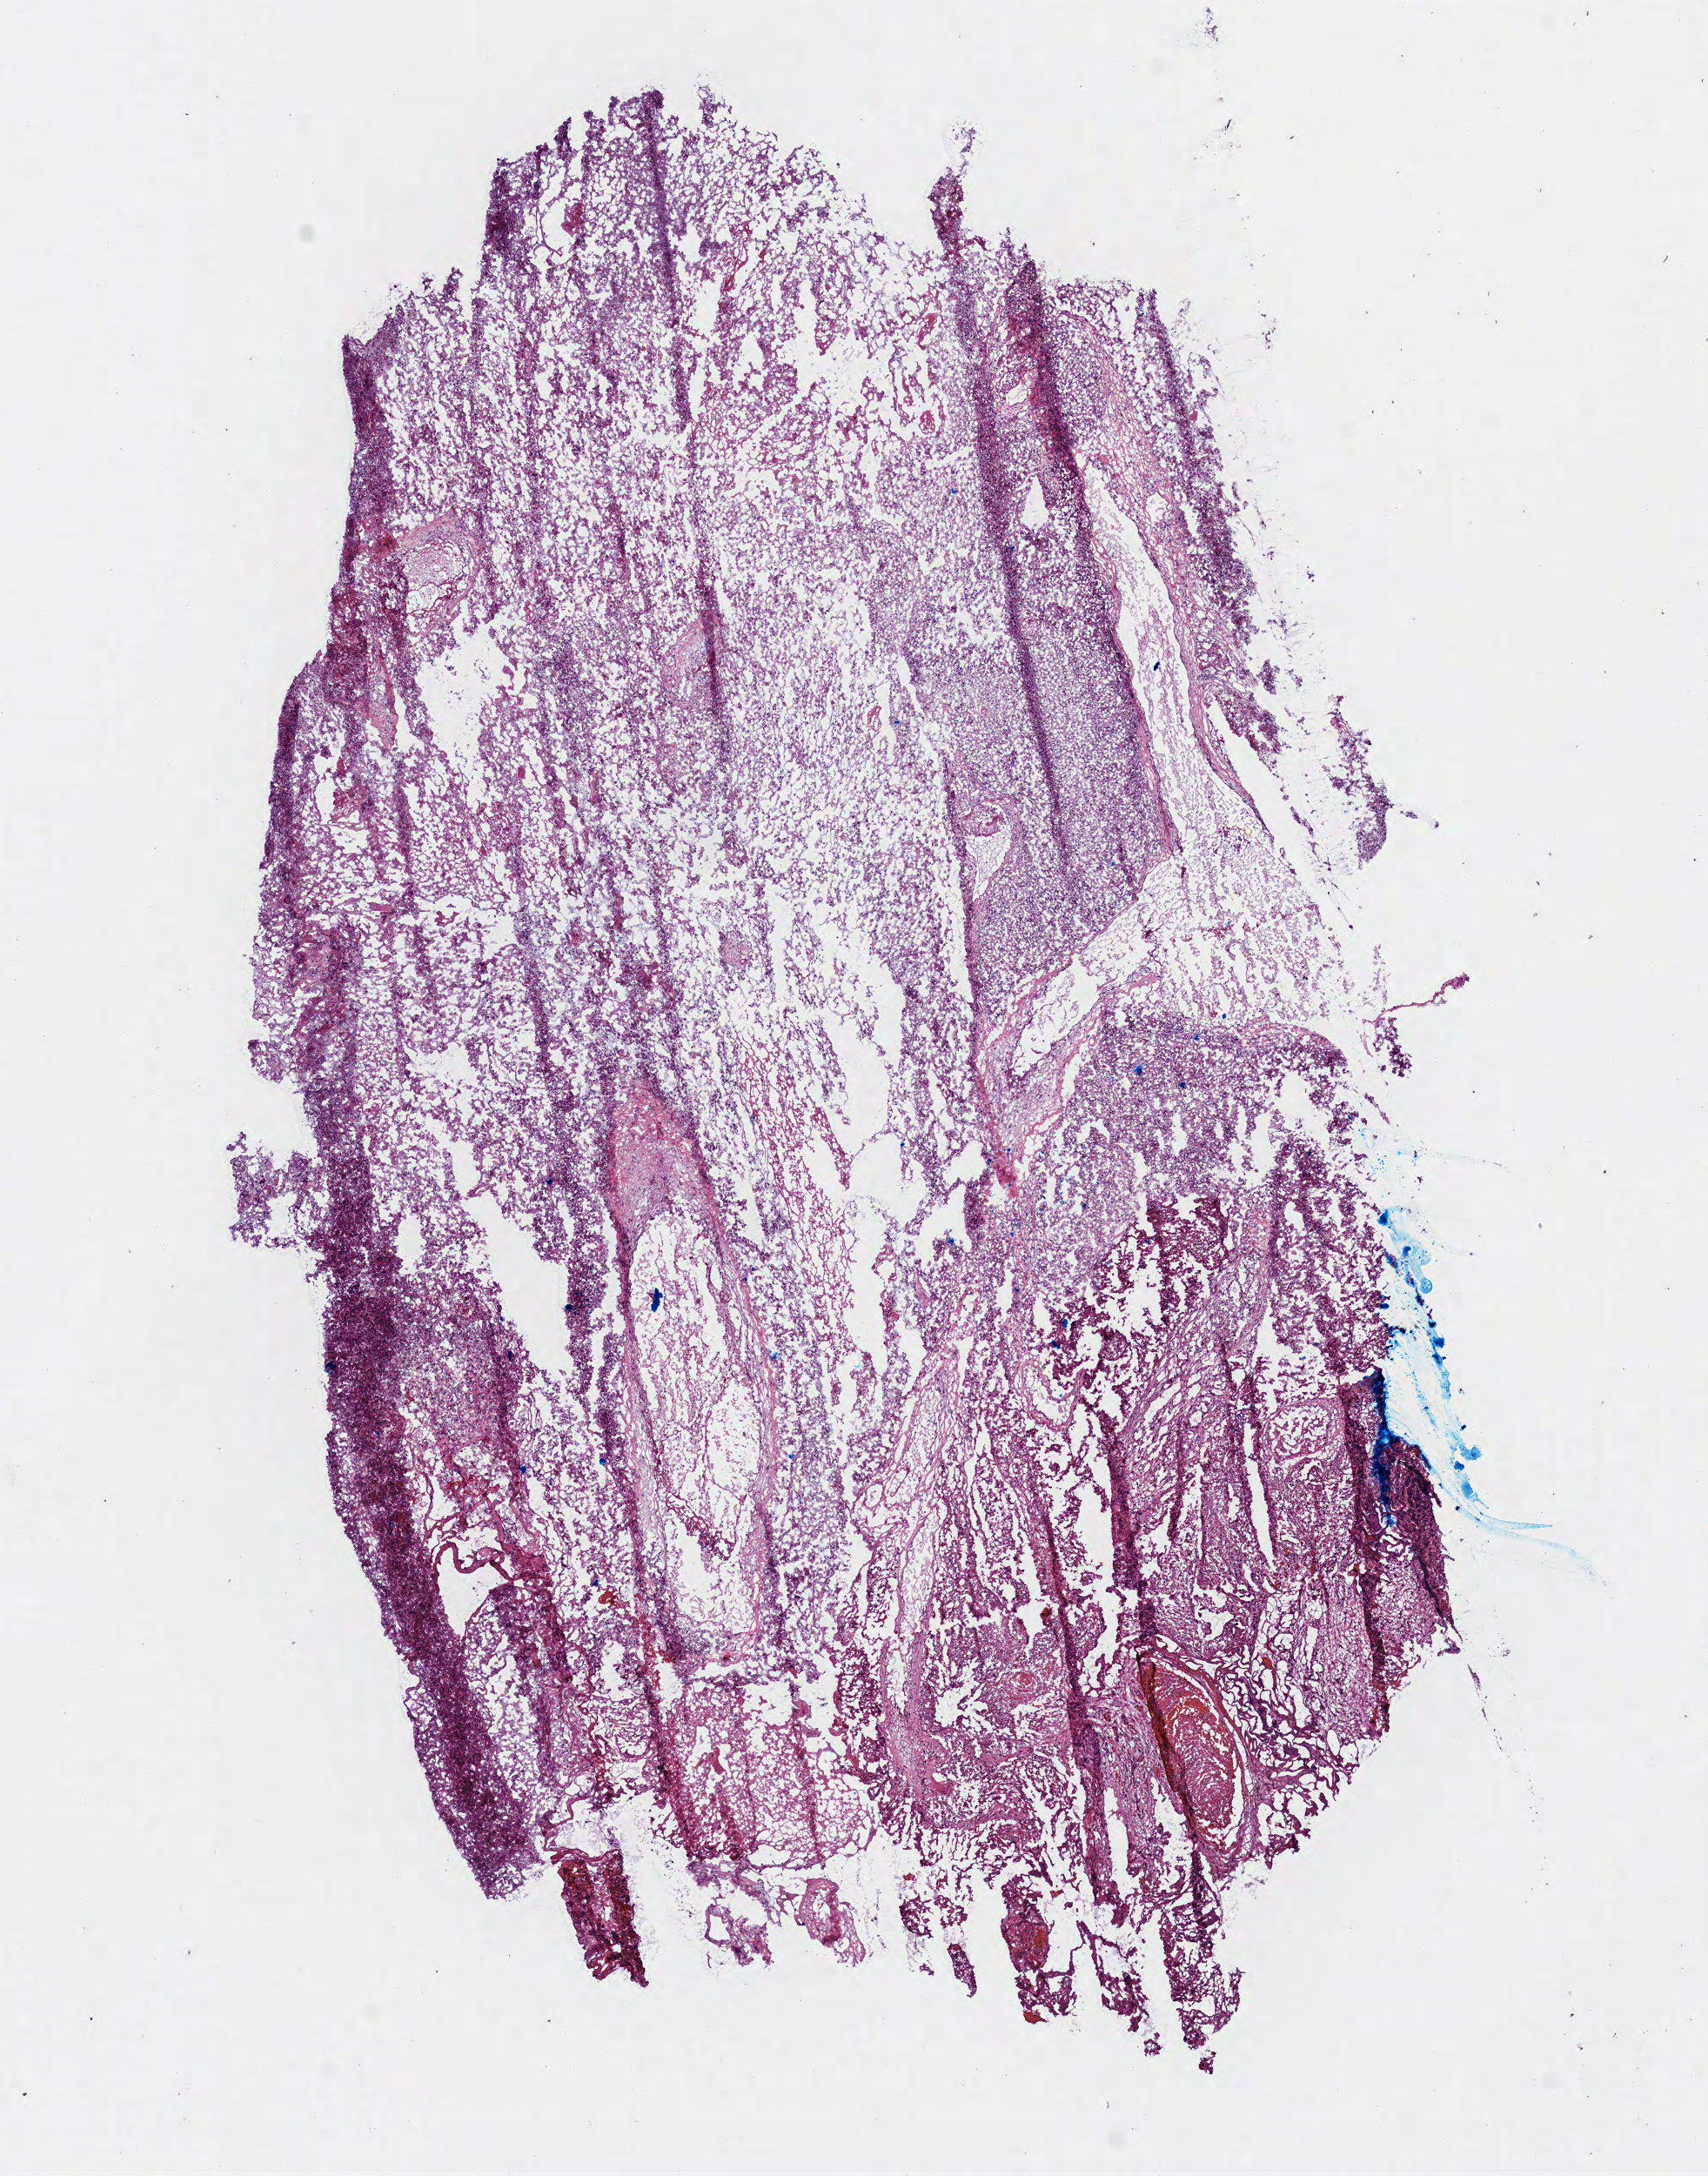
Whole-slide histology image, Hematoxylin and eosin (H&E) stained — shown as a low-resolution overview of the whole scanned area (about 7.7 x 9.9 mm), frozen section, brain, primary tumour sample. Patient: male, age at initial diagnosis 62 years. Composition of this section per pathologist review: tumour cells 95%, tumour nuclei 70%, normal cells 0%, stromal cells 5%, necrosis 0%.
Pathologic diagnosis: Glioblastoma.